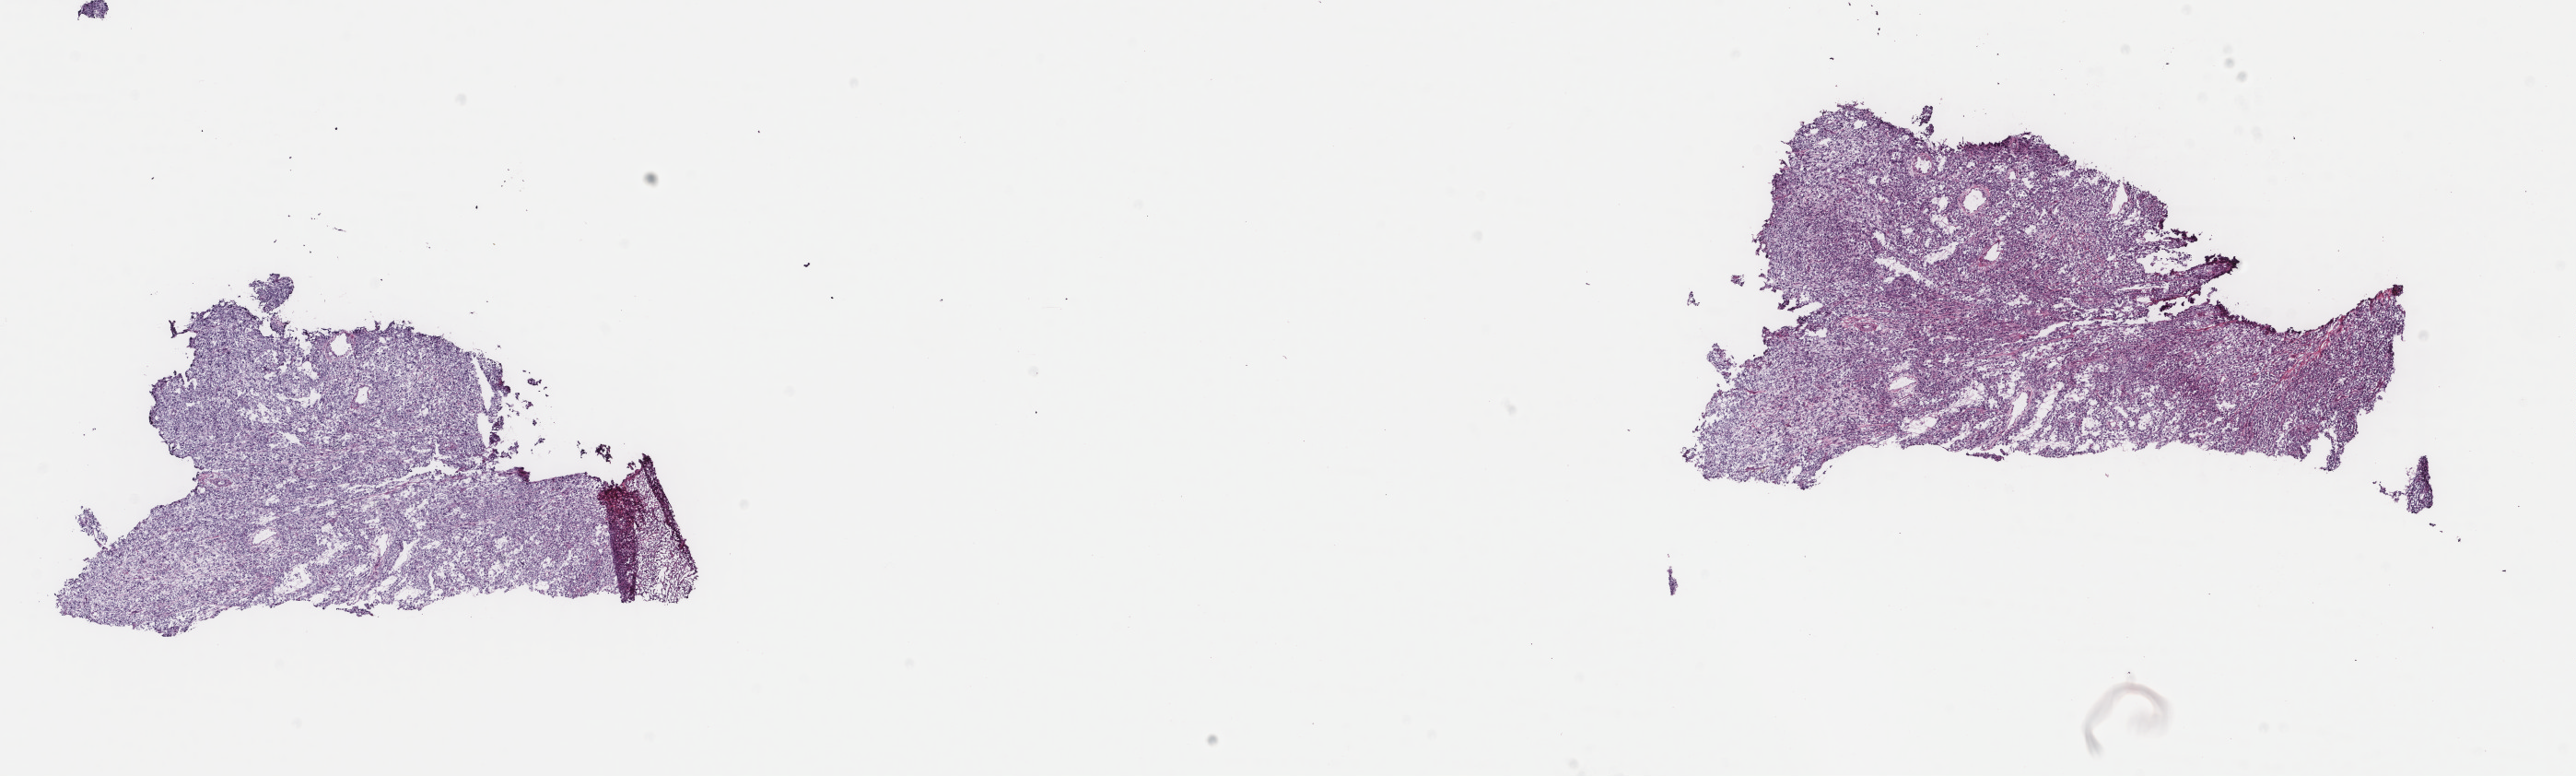
Digitized H&E tissue section (whole slide) — low-resolution overview of the scanned area, about 22.2 x 6.7 mm. Frozen section from the top of the tissue portion. Metastatic tumour sample. Female patient; age at initial diagnosis 83 years. Composition of this section per pathologist review: tumour cells 100%, tumour nuclei 80%, normal cells 0%, stromal cells 0%, necrosis 0%. Infiltration values recorded for this section: lymphocyte infiltration 0%, monocyte infiltration 0%, neutrophil infiltration 0%.
This section: metastatic tumour tissue. Patient diagnosis: Malignant melanoma, NOS.